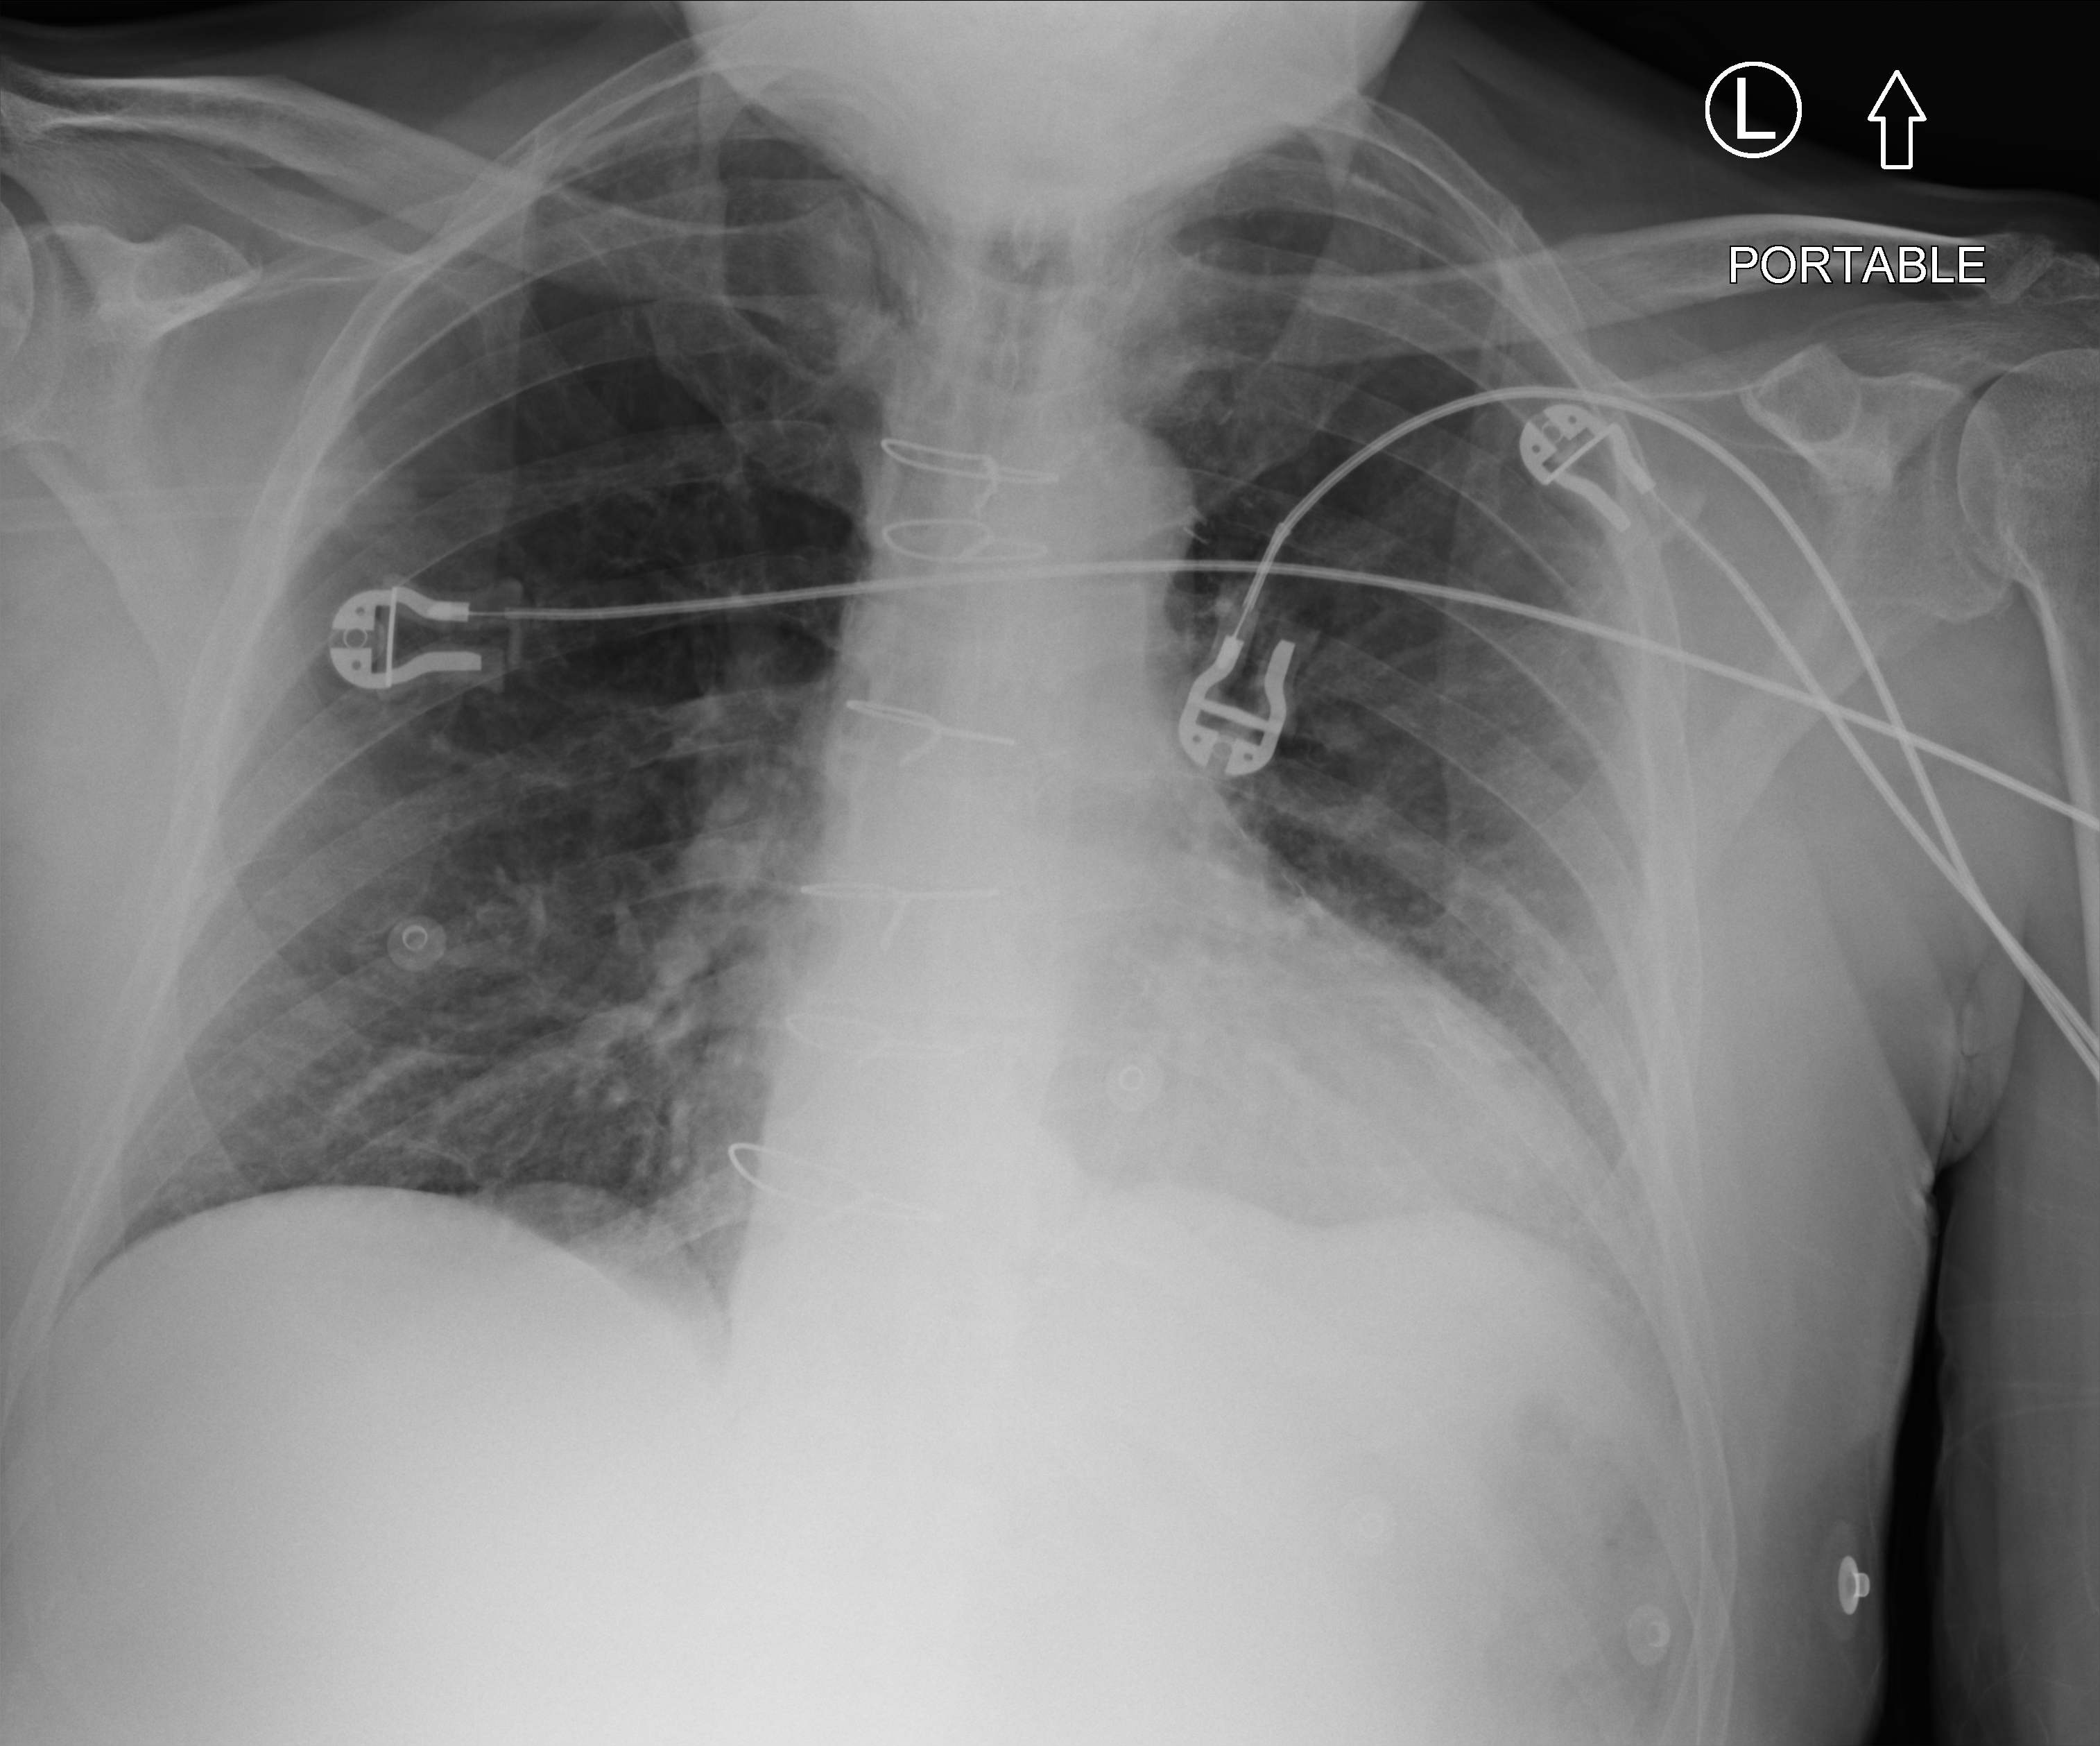
Chest X-ray (portable); anteroposterior (AP) projection. Male patient hospitalised with COVID-19, age 75–90 years.
Admission-level facts for this patient (not findings on this image; timing relative to this image not recorded): other chronic lung disease (admission record): yes; mechanically ventilated during this hospital stay: no; admitted to intensive care during this hospital stay: no.